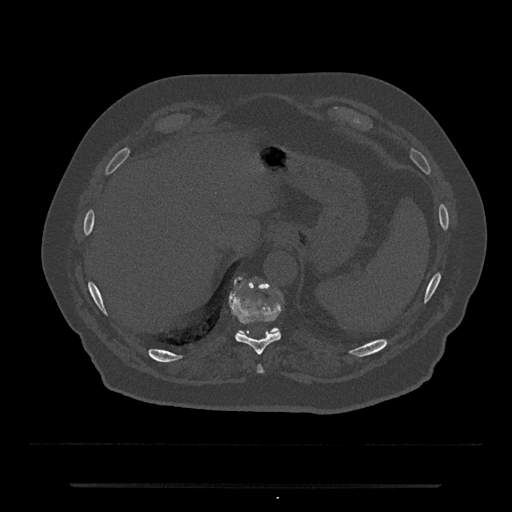
CT including the spine, one axial slice; position 694 of 797 along the scan axis; 120 kVp; bone window (W 1800 / L 400 HU); 0.5 mm slice thickness; 512 × 512 image matrix. Male patient, age 80 years. From the clinical record (not read from this slice): primary cancer: prostate; vertebrae with lytic lesions (as recorded): L1, T11.
Annotated regions visible in this slice (semi-automatically segmented with operator editing):
- T10 vertebra: bounding box [x1, y1, x2, y2] px = [229, 278, 281, 355]
- T11 vertebra: [239, 327, 280, 333]
- T9 vertebra: [257, 365, 263, 373]